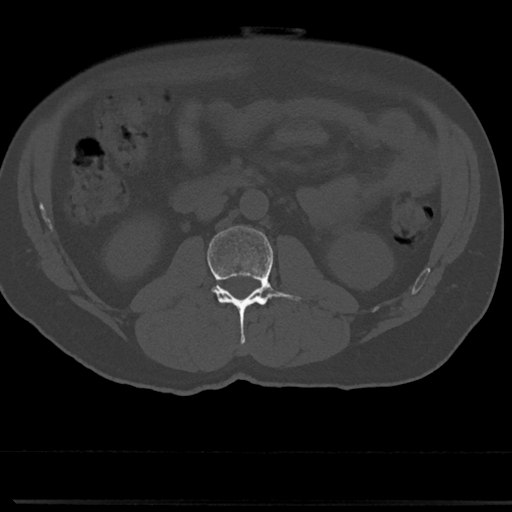
CT including the spine, one axial slice. Position 10 of 817 along the scan axis. Bone window (W 1800 / L 400 HU). 512 × 512 image matrix. Male patient, age 61 years. From the clinical record (not read from this slice): primary cancer: prostate.
Annotated regions visible in this slice (semi-automatically segmented with operator editing):
- L2 vertebra: bounding box (x1, y1, x2, y2) in pixels: (207, 226, 301, 345)